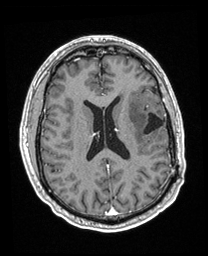
Brain MRI from a brain-tumour surgery series, one axial slice. Slice 93 of 208 in the series (ordered by position). T1-weighted post-contrast. 1 mm slice thickness. 208 × 256 image matrix, field of view 211 × 260 mm. Case-level facts recorded for this patient, not image findings: histopathology: Astrocytoma; WHO grade: 3; IDH mutation: yes.
Outlined on this slice (expert manual segmentation):
- previous resection cavity: bounding box (x1, y1, x2, y2) in pixels: (144, 113, 165, 134)